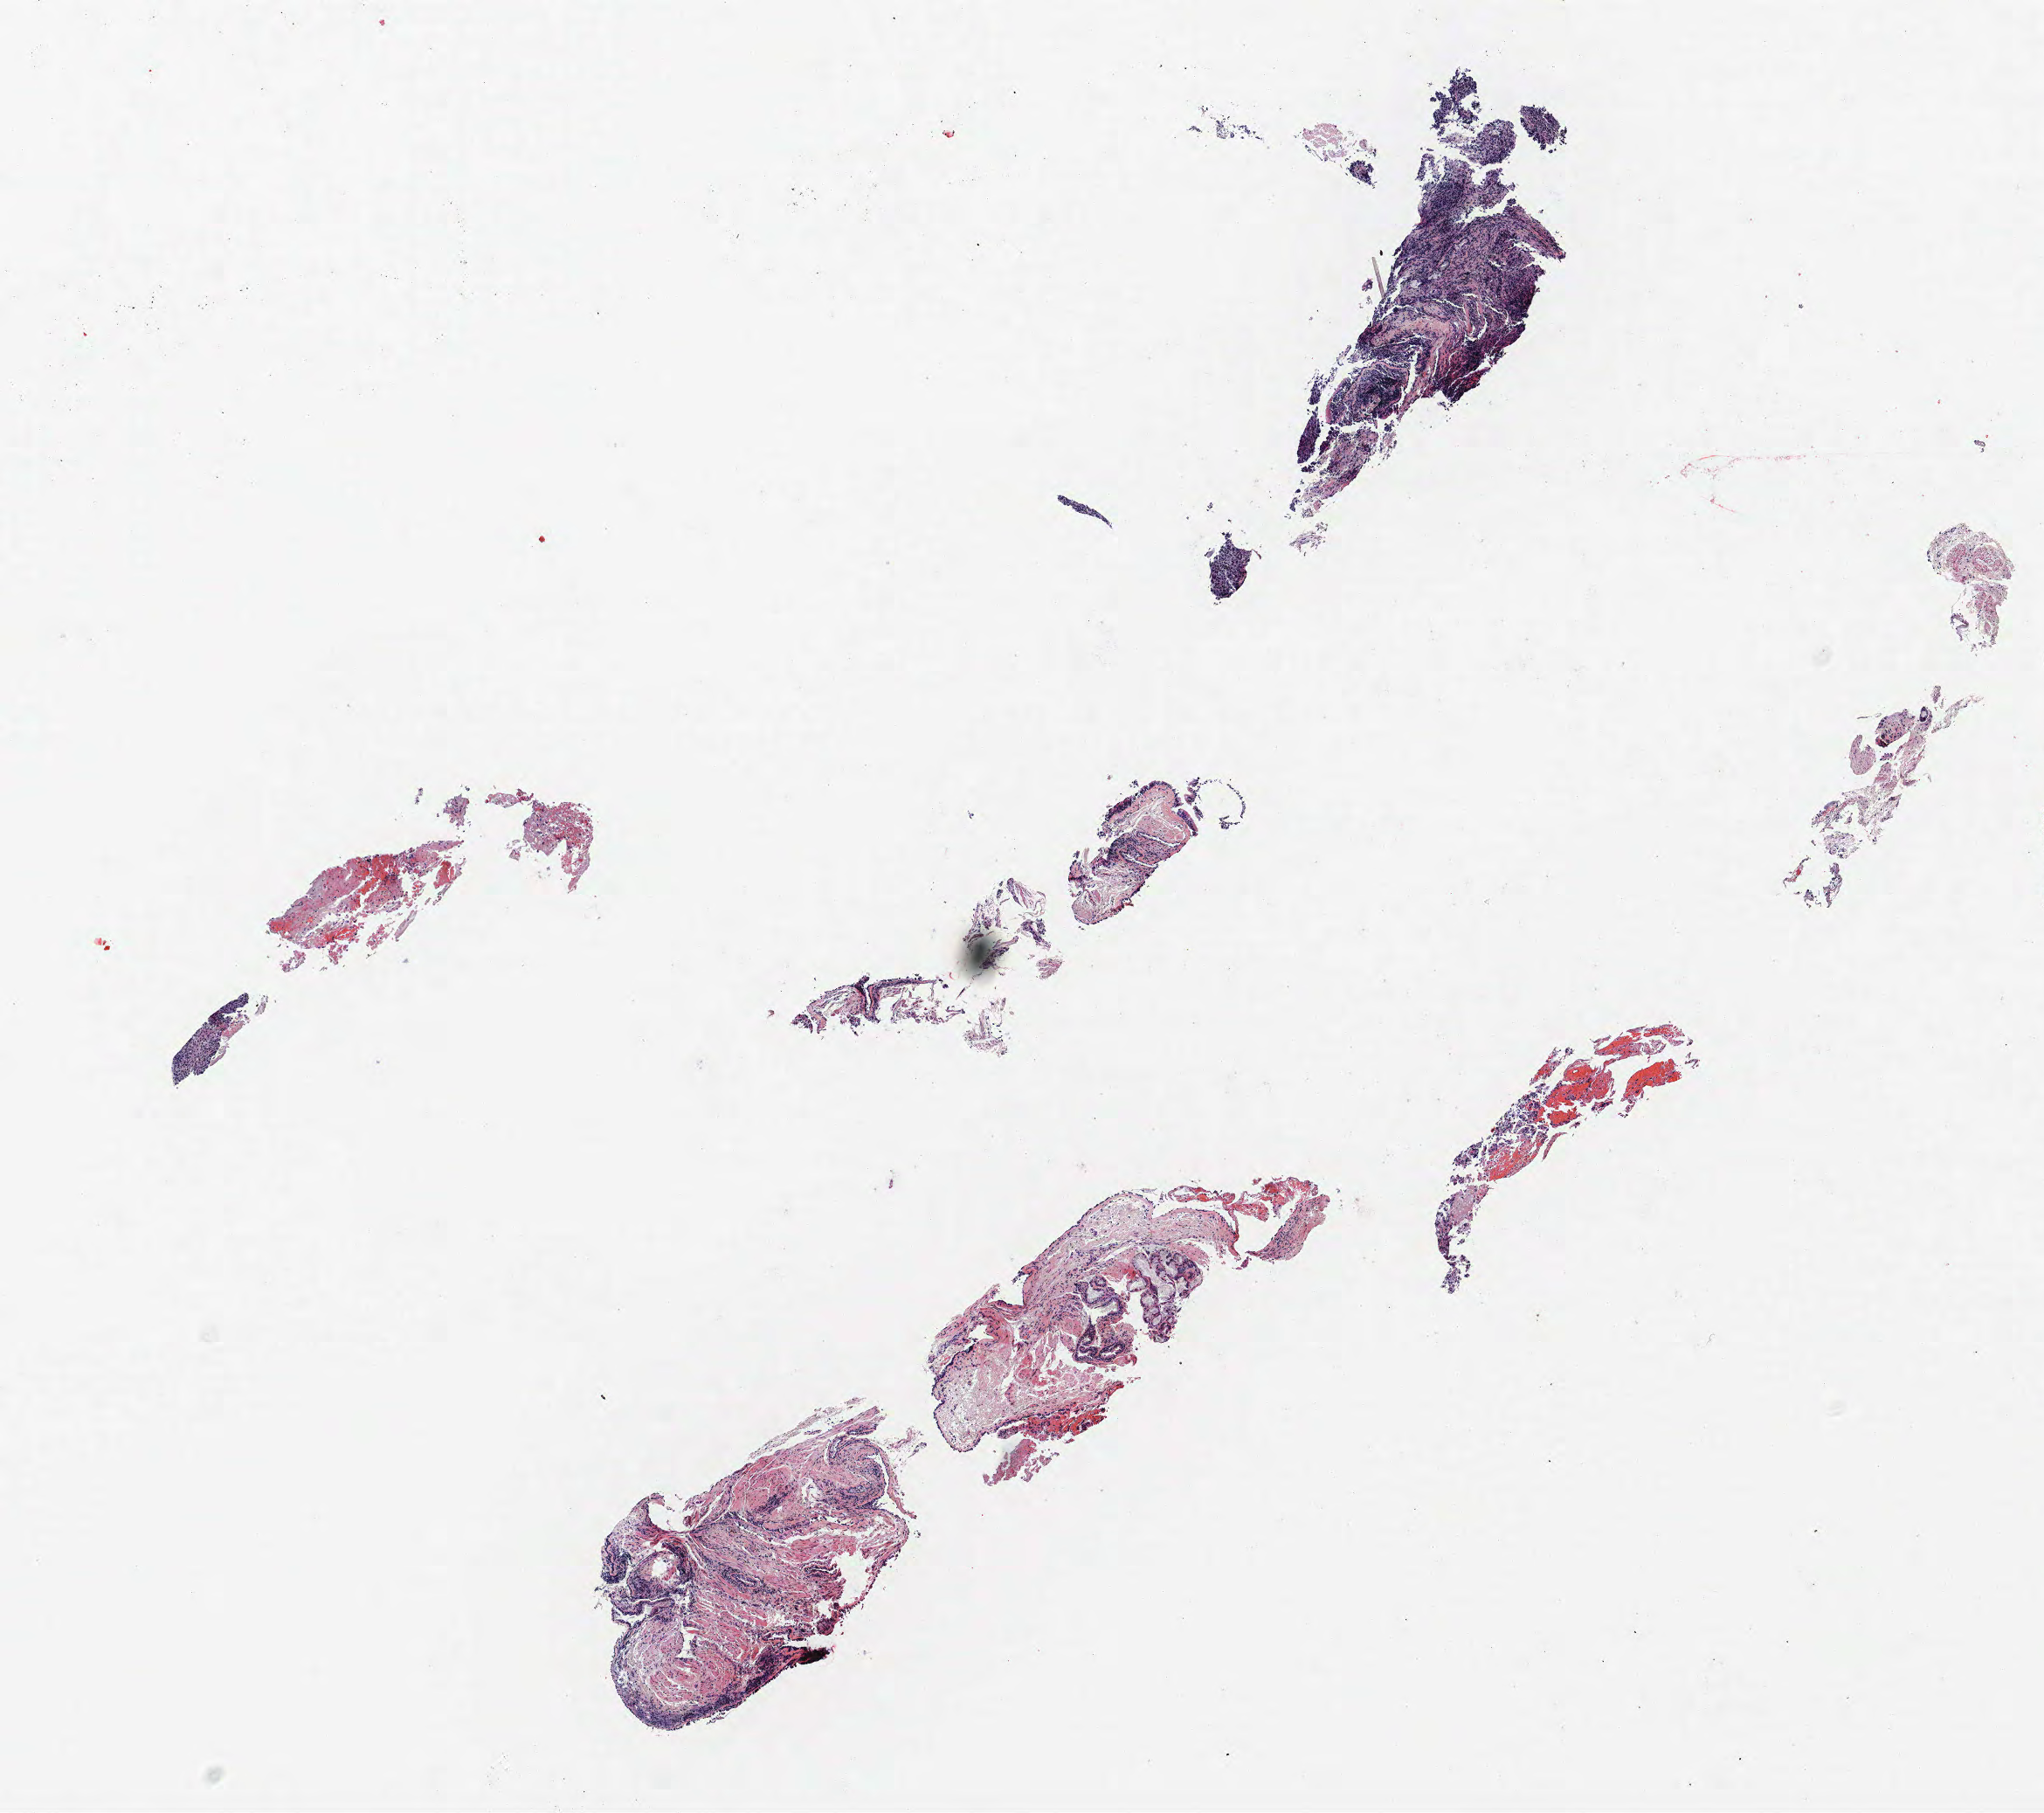
H&E-stained whole-slide image, whole scanned area (about 9.4 x 8.3 mm, from a 40x scan) shown as a low-resolution overview, FFPE section, lung tissue. Male, age 65 at enrolment. Current smoker at enrolment. Grade: poorly differentiated (G3).
- primary tumour location (clinical record): right lower lobe
- stage (AJCC 6th edition): IB
- ICD-O-3 topography: lower lobe of lung (C34.3)
- tumour size (pathology): 50 mm
- participant's lung-cancer diagnosis: Squamous cell carcinoma, NOS